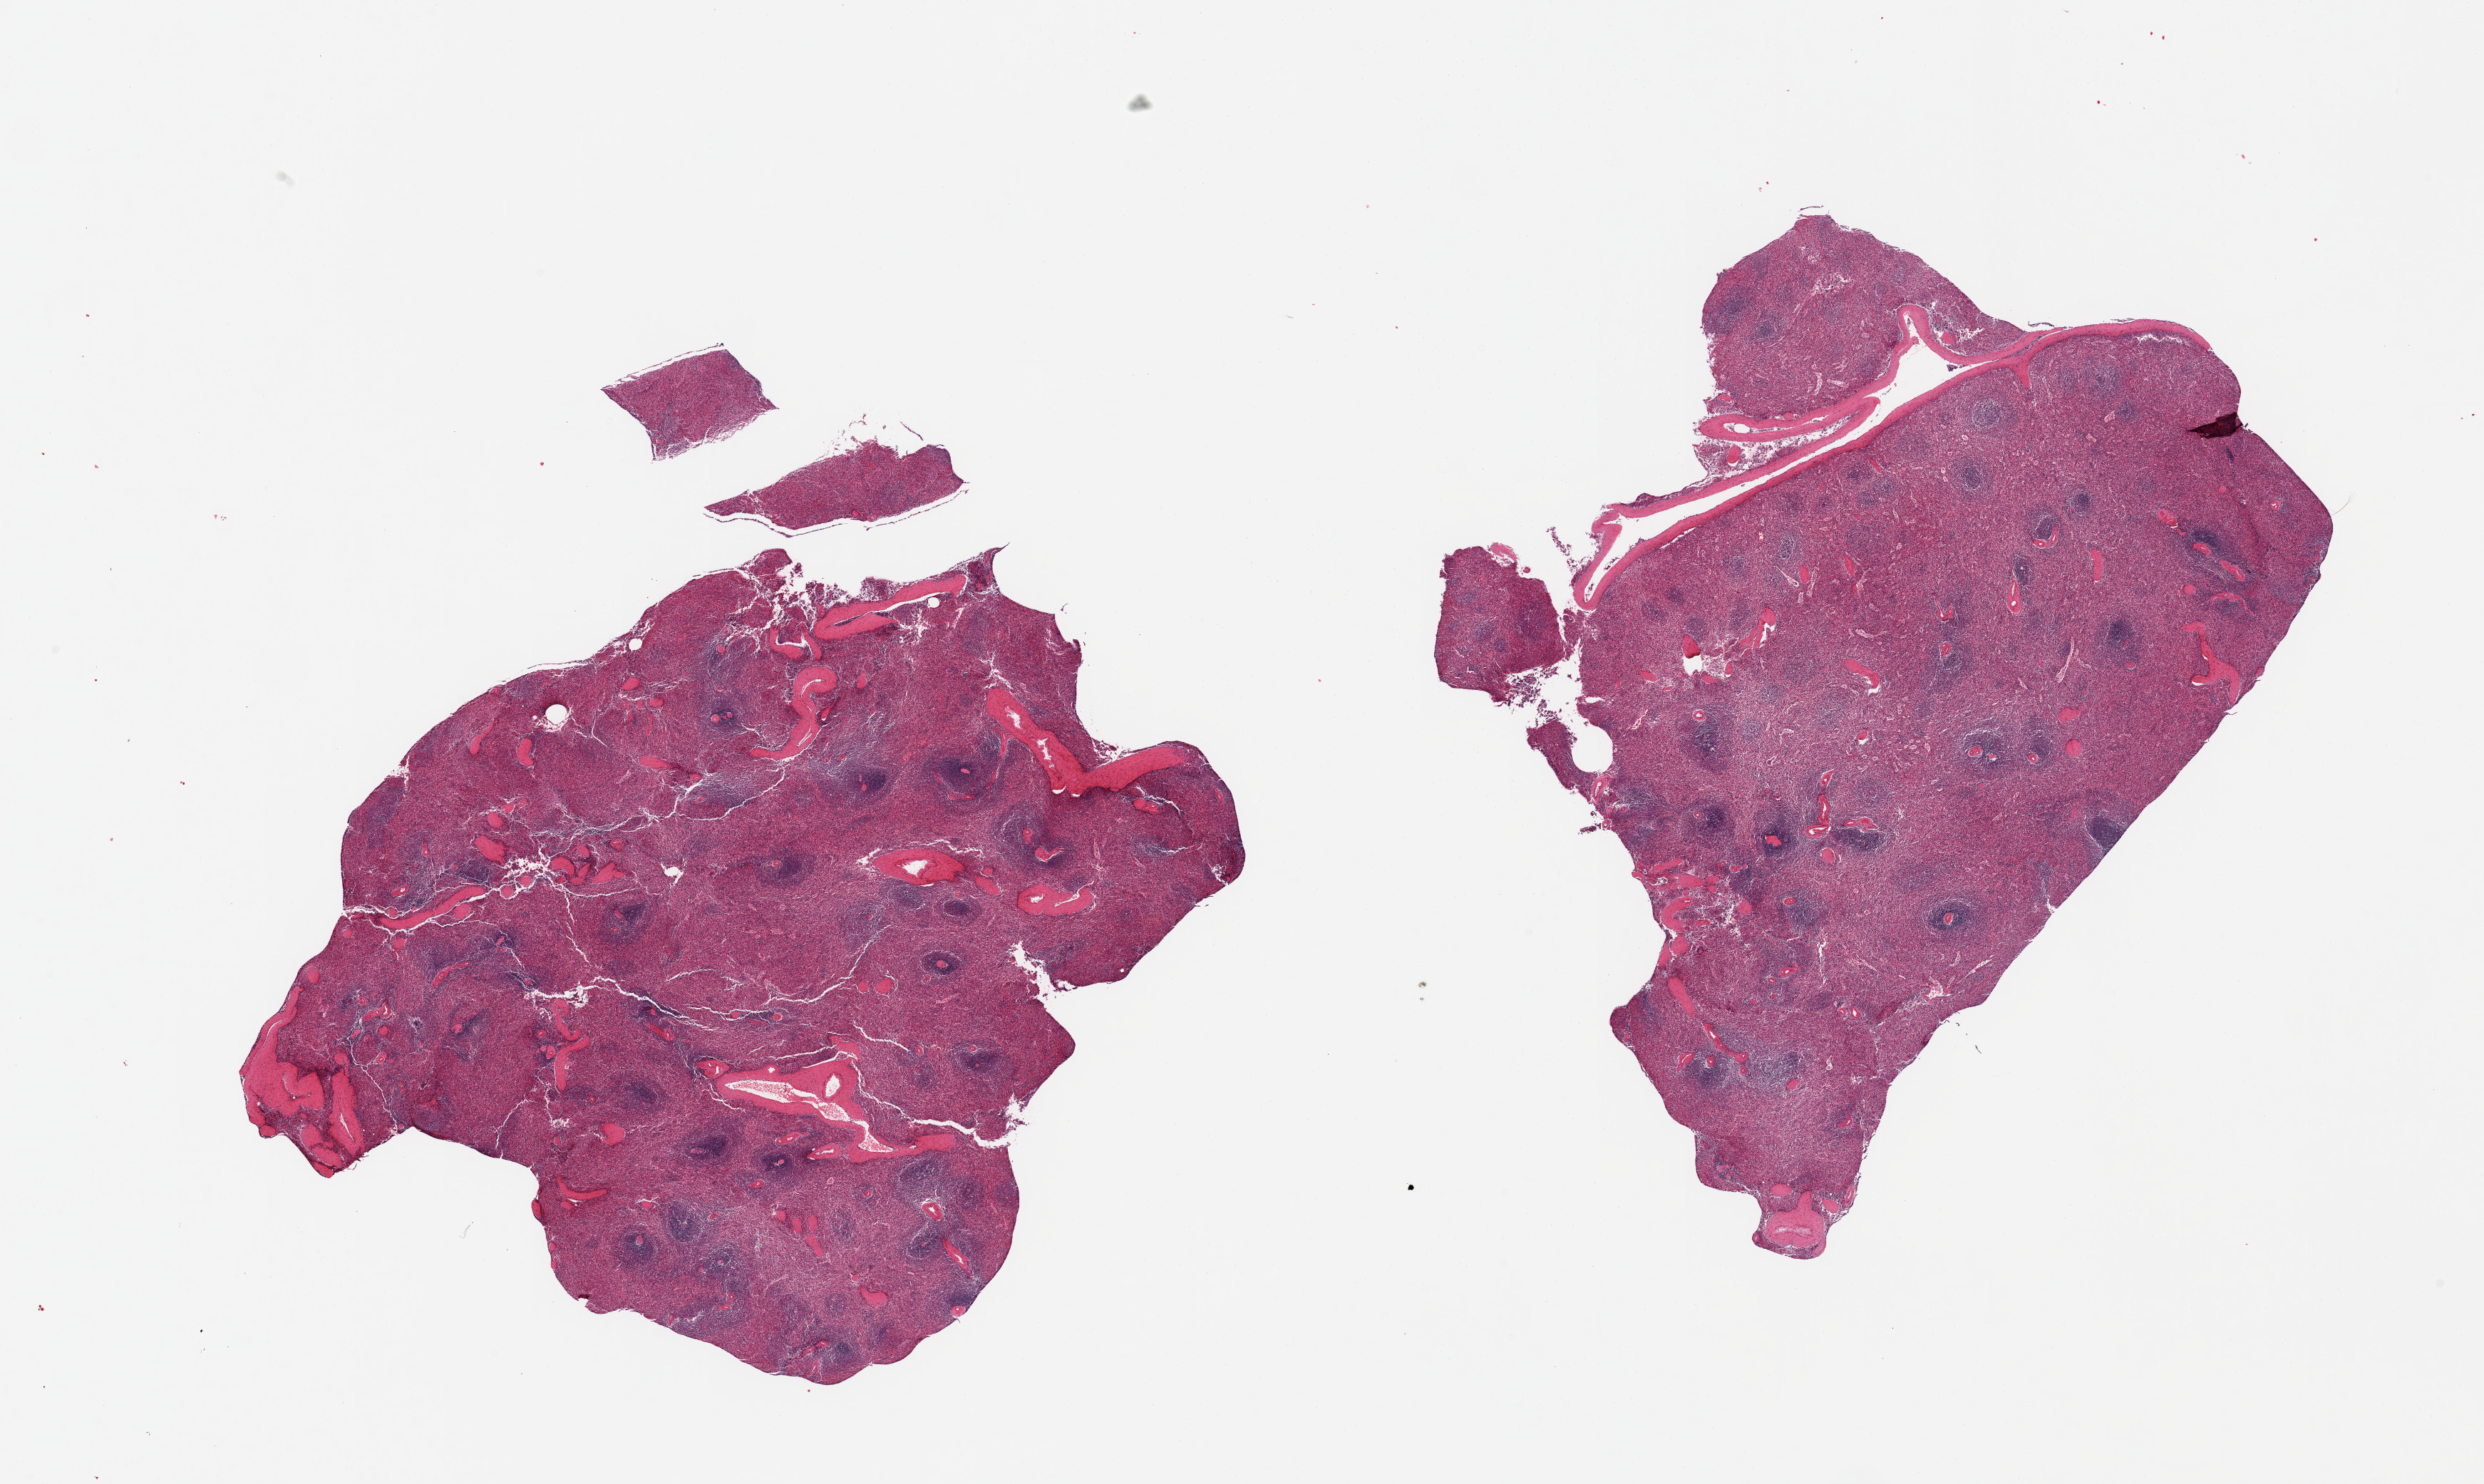
Digitized hematoxylin and eosin (H&E)-stained section — a low-resolution overview of the entire scanned area, about 27.6 x 16.5 mm (from a 20x scan), PAXgene-fixed, paraffin-embedded tissue, section of spleen (target tissue), tissue donor sample. Donor sex: male.
- reviewer comment on this tissue sample: 2 pieces, no abnormalities